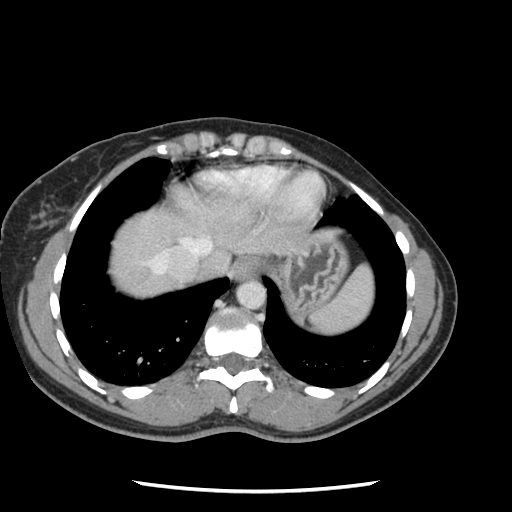
Contrast-enhanced abdominal CT, one axial slice. Position 110 of 134 along the scan axis. 120 kVp. Intravenous contrast given. Soft-tissue window (W 400 / L 40 HU). 2.5 mm slice thickness. 512 × 512 image matrix, field of view 330 × 330 mm. Female patient, age 43 years. From the clinical record (not read from this slice): diagnosis: colorectal cancer liver metastases, imaged before liver resection; multiple liver metastases: yes; largest metastasis: 3.4 cm; disease in both lobes: yes.
Annotated regions visible in this slice (expert manual segmentation):
- hepatic veins: box from (x=150, y=238) to (x=212, y=274) px
- liver: (x=111, y=208)–(x=199, y=296)
- planned liver remnant (the part of the liver to remain after resection): (x=112, y=208)–(x=194, y=287)